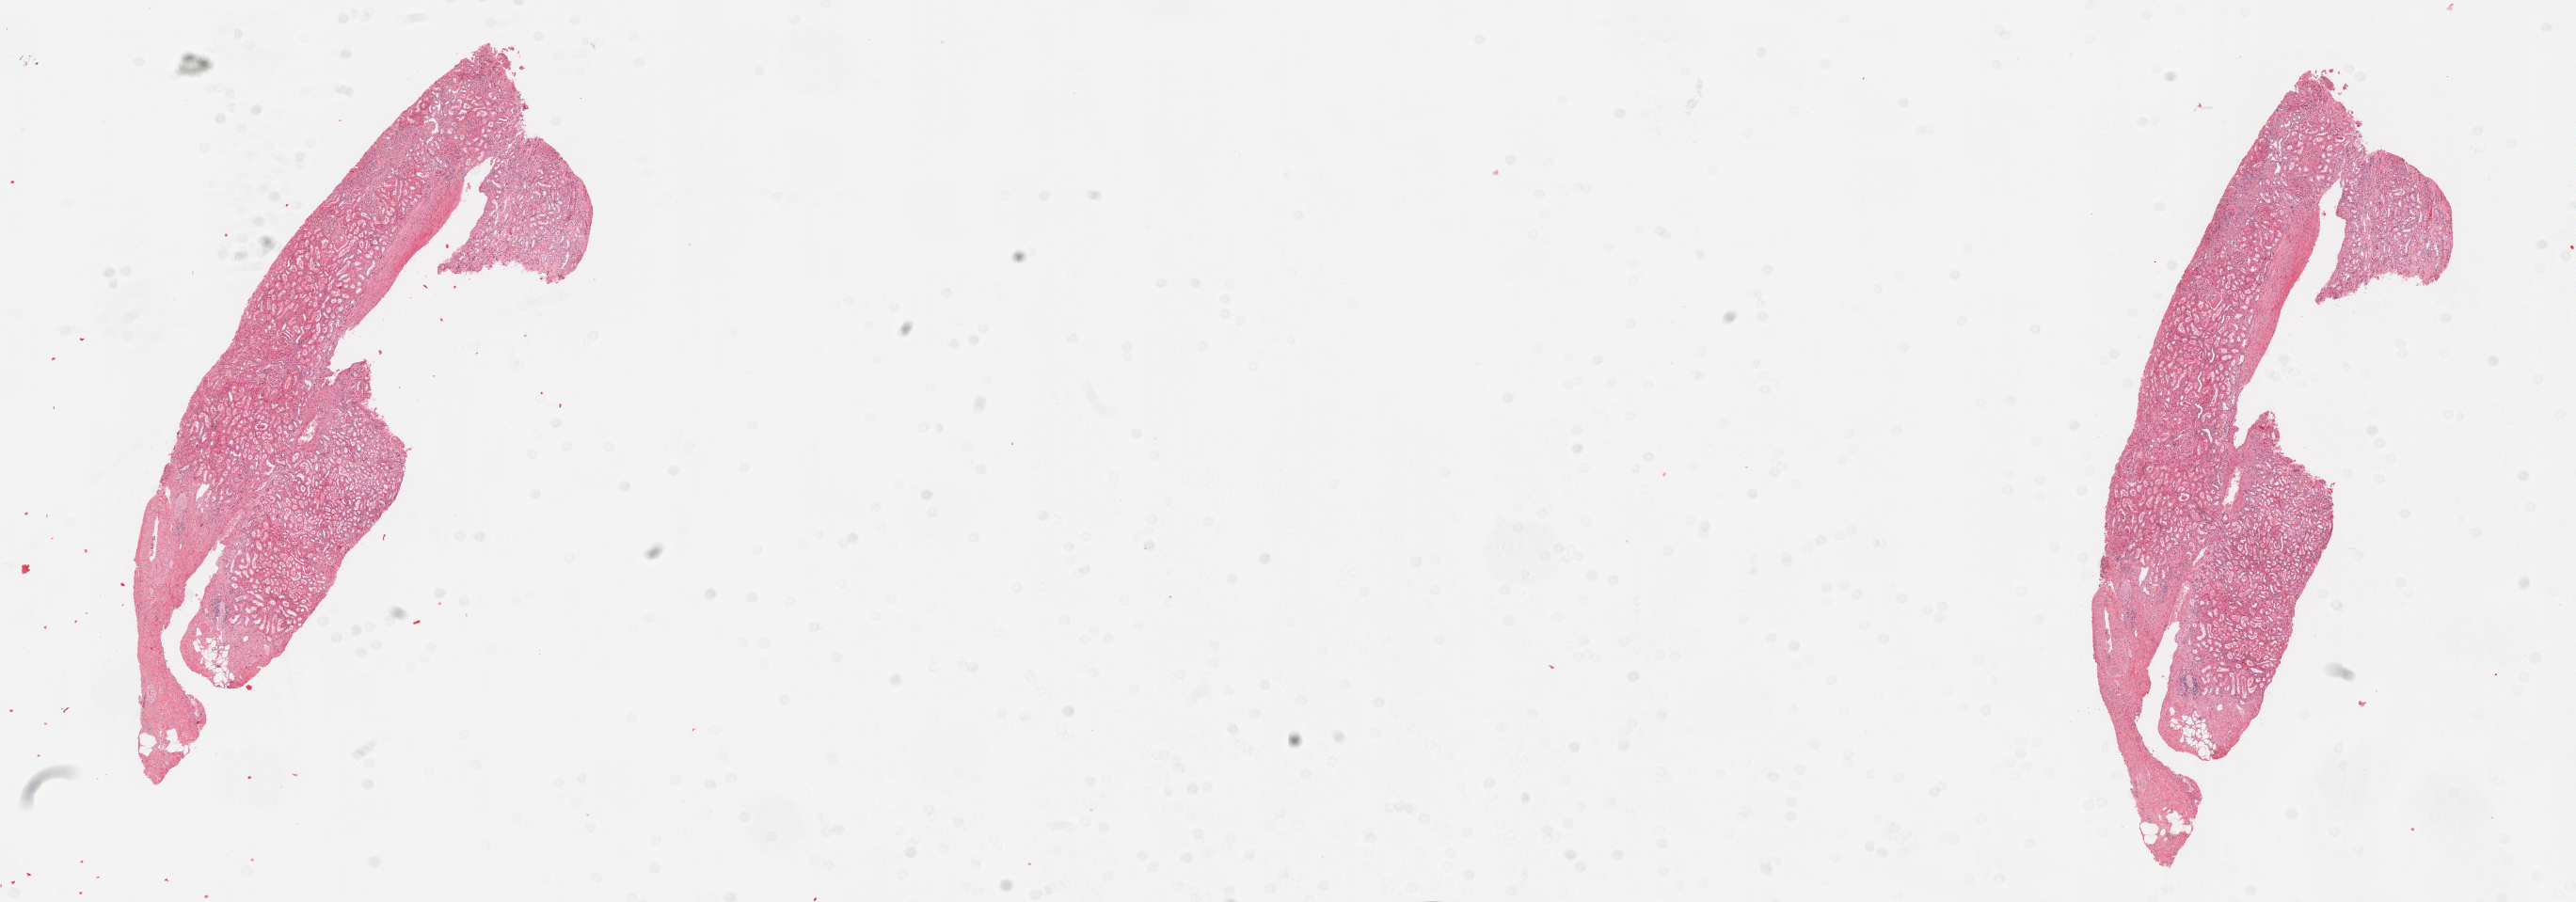
H&E-stained whole-slide image — whole scanned area (about 21.7 x 7.6 mm, from a 20x scan) shown as a low-resolution overview, kidney, normal (non-tumour) tissue. Male, 46 y/o.
This section: normal (non-tumour) tissue from the same patient. Patient diagnosis: Renal cell carcinoma, NOS.